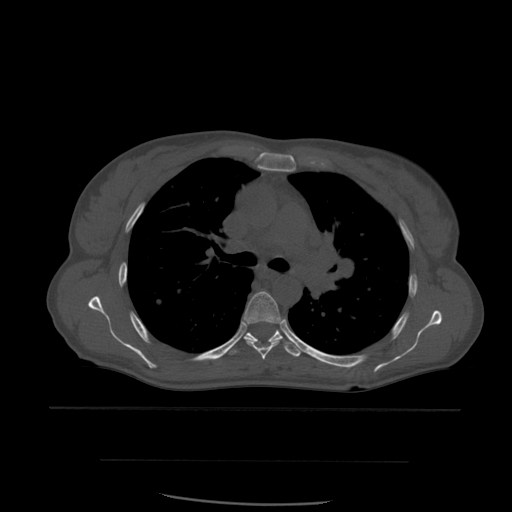
CT including the spine, one axial slice; position 403 of 574 along the scan axis; bone window (W 1800 / L 400 HU); 512 × 512 image matrix, field of view 392 × 392 mm. Patient age 48 years. From the clinical record (not read from this slice): primary cancer: lung; vertebrae with lytic lesions (as recorded): T11.
Annotated regions visible in this slice (semi-automatically segmented with operator editing):
- T5 vertebra: bounding box (x1, y1, x2, y2) in pixels: (244, 292, 284, 360)
- T6 vertebra: (226, 330, 302, 357)